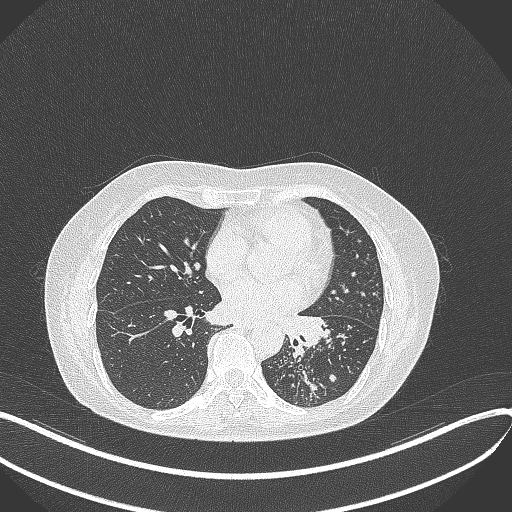
Chest CT, one axial slice. Position 183 of 429 along the scan axis. Reconstruction kernel B70f. 100 kVp. Lung window (W 1500 / L -600 HU). 512 × 512 image matrix, field of view 400 × 400 mm. Female patient, age 63 years. From the clinical record (not read from this slice): clinical TNM (as recorded): T1b N0 M0; histopathological grade: G2-3.
Outlined on this slice (rectangle marked by the reading radiologist):
- lung tumour (recorded histology: adenocarcinoma): bounding box (x1, y1, x2, y2) in pixels: (278, 308, 327, 351)